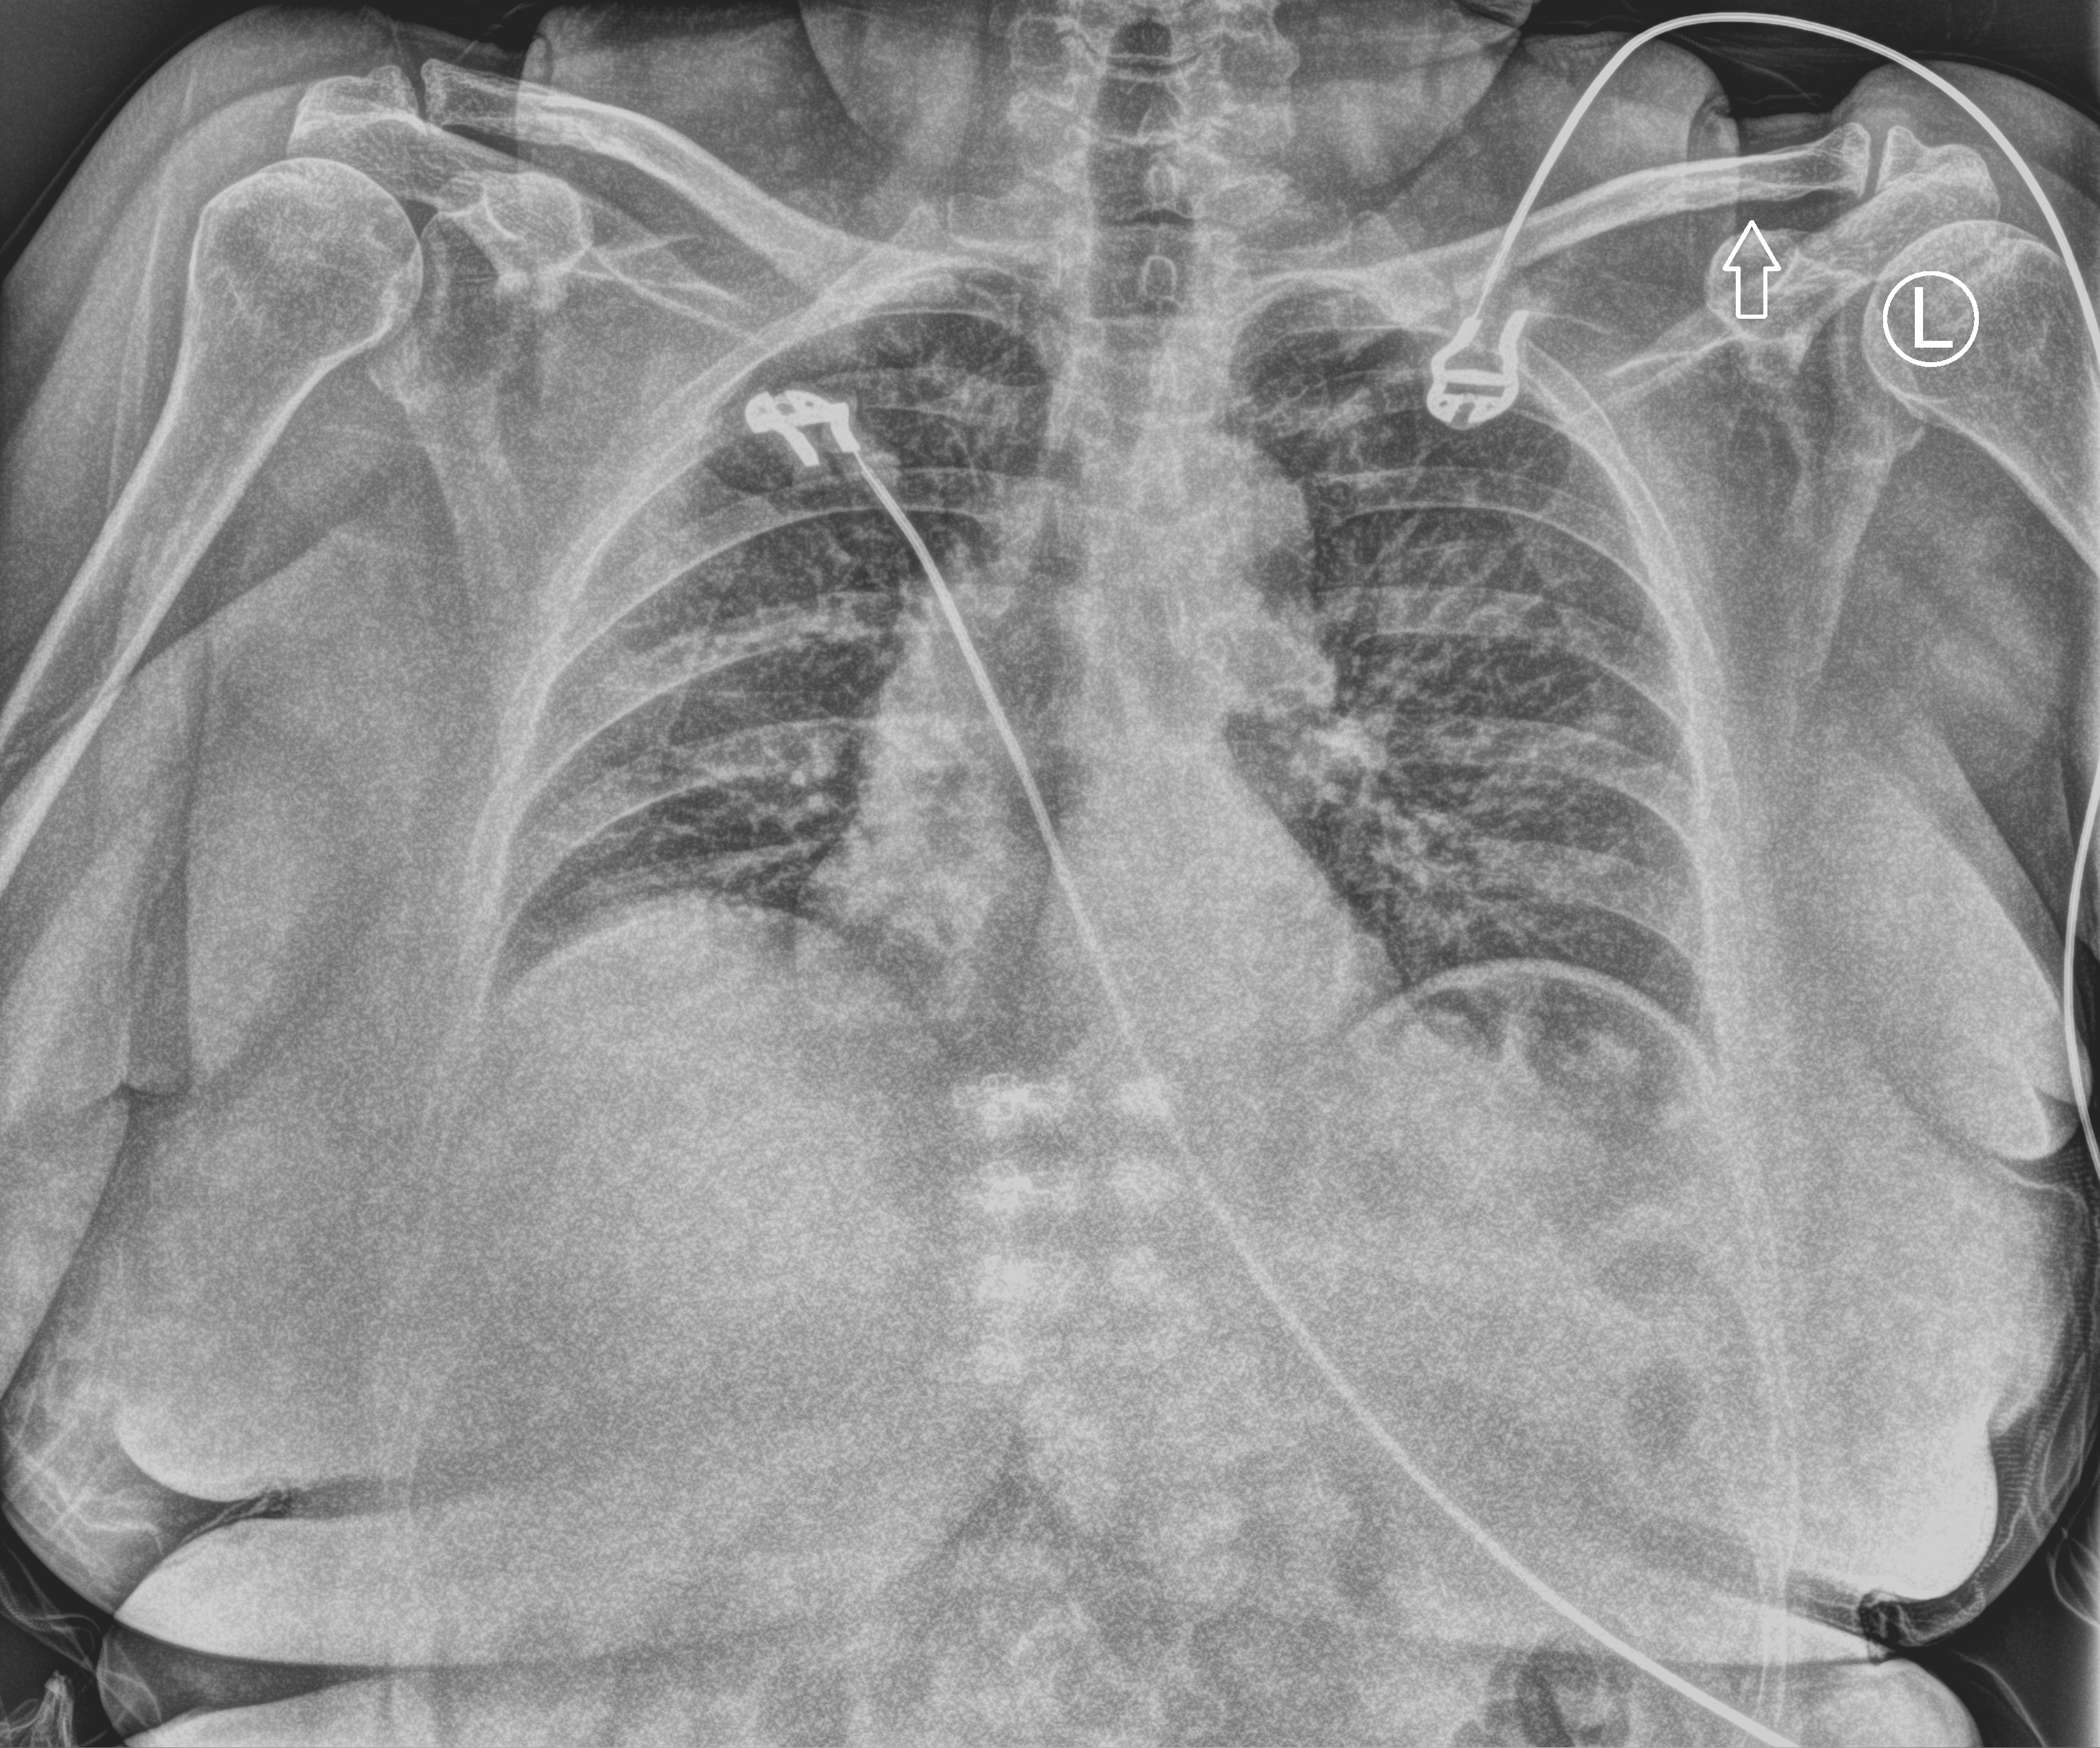
Bedside chest radiograph (computed radiography); anteroposterior (AP) projection. Patient hospitalised with COVID-19; female, aged 60–74 years.
Hospital-stay facts (about this admission, not read from this image; timing relative to this image not recorded): admitted to intensive care during this hospital stay: no.